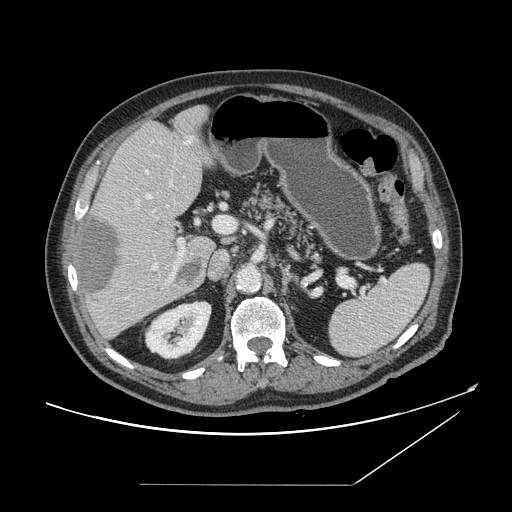
Contrast-enhanced abdominal CT, one axial slice; slice 92 of 166 in the series (ordered by position); 120 kVp; intravenous contrast given; soft-tissue window (W 400 / L 40 HU); 2.5 mm slice thickness; 512 × 512 image matrix, field of view 416 × 416 mm. Male patient, age 80 years. Case-level facts recorded for this patient, not image findings: diagnosis: colorectal cancer liver metastases, imaged before liver resection; multiple liver metastases: no; largest metastasis: 2.2 cm; disease in both lobes: no.
Outlined on this slice (outlined manually by an expert reader):
- hepatic veins: box from (x=146, y=170) to (x=173, y=270) px
- liver: (x=76, y=107)–(x=217, y=339)
- planned liver remnant (the part of the liver to remain after resection): (x=96, y=106)–(x=218, y=251)
- portal vein (with intrahepatic branches): (x=137, y=200)–(x=231, y=277)
- liver metastasis: (x=84, y=218)–(x=201, y=296)